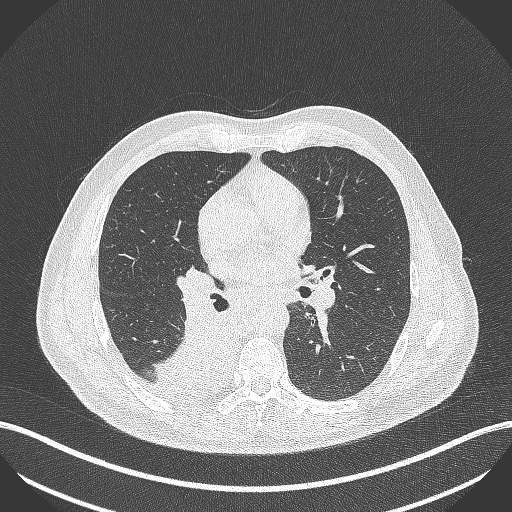
Chest CT, one axial slice; position 255 of 451 along the scan axis; reconstruction kernel B70f; 100 kVp; lung window (W 1500 / L -600 HU); 512 × 512 image matrix. Male patient, age 61 years. Case-level facts recorded for this patient, not image findings: clinical TNM (as recorded): T1 N0 M0; histopathological grade: G3.
Structures marked on this image (bounding box drawn by a radiologist):
- lung tumour (recorded histology: small cell carcinoma): bounding box <149,311,239,407> (left, top, right, bottom; pixels)